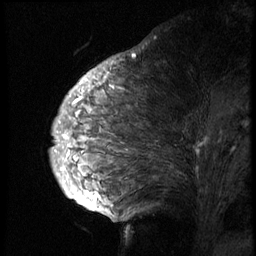
Breast MRI (dynamic contrast-enhanced), one sagittal slice. Slice 30 of 74 in the series (ordered by position). 3 images stored at this slice position (order not interpretable as contrast timing). 1.5 T. TE 4.2 ms, TR 8.9 ms. 2.5 mm slice thickness. 256 × 256 image matrix, field of view 200 × 200 mm. Female patient, age 57 years. From the clinical record (not read from this slice): setting: breast cancer imaged before/during neoadjuvant chemotherapy; receptor status: HER2-positive.
Structures marked on this image (semi-automatic segmentation, software-assisted and operator-edited):
- analysis volume of interest (the breast-tissue region the enhancement analysis was run in; not a lesion): bounding box [x1, y1, x2, y2] px = [51, 67, 248, 173]
- tumour enhancement mask (voxels above the 140 % enhancement threshold inside the analysis volume of interest): [74, 85, 207, 146]